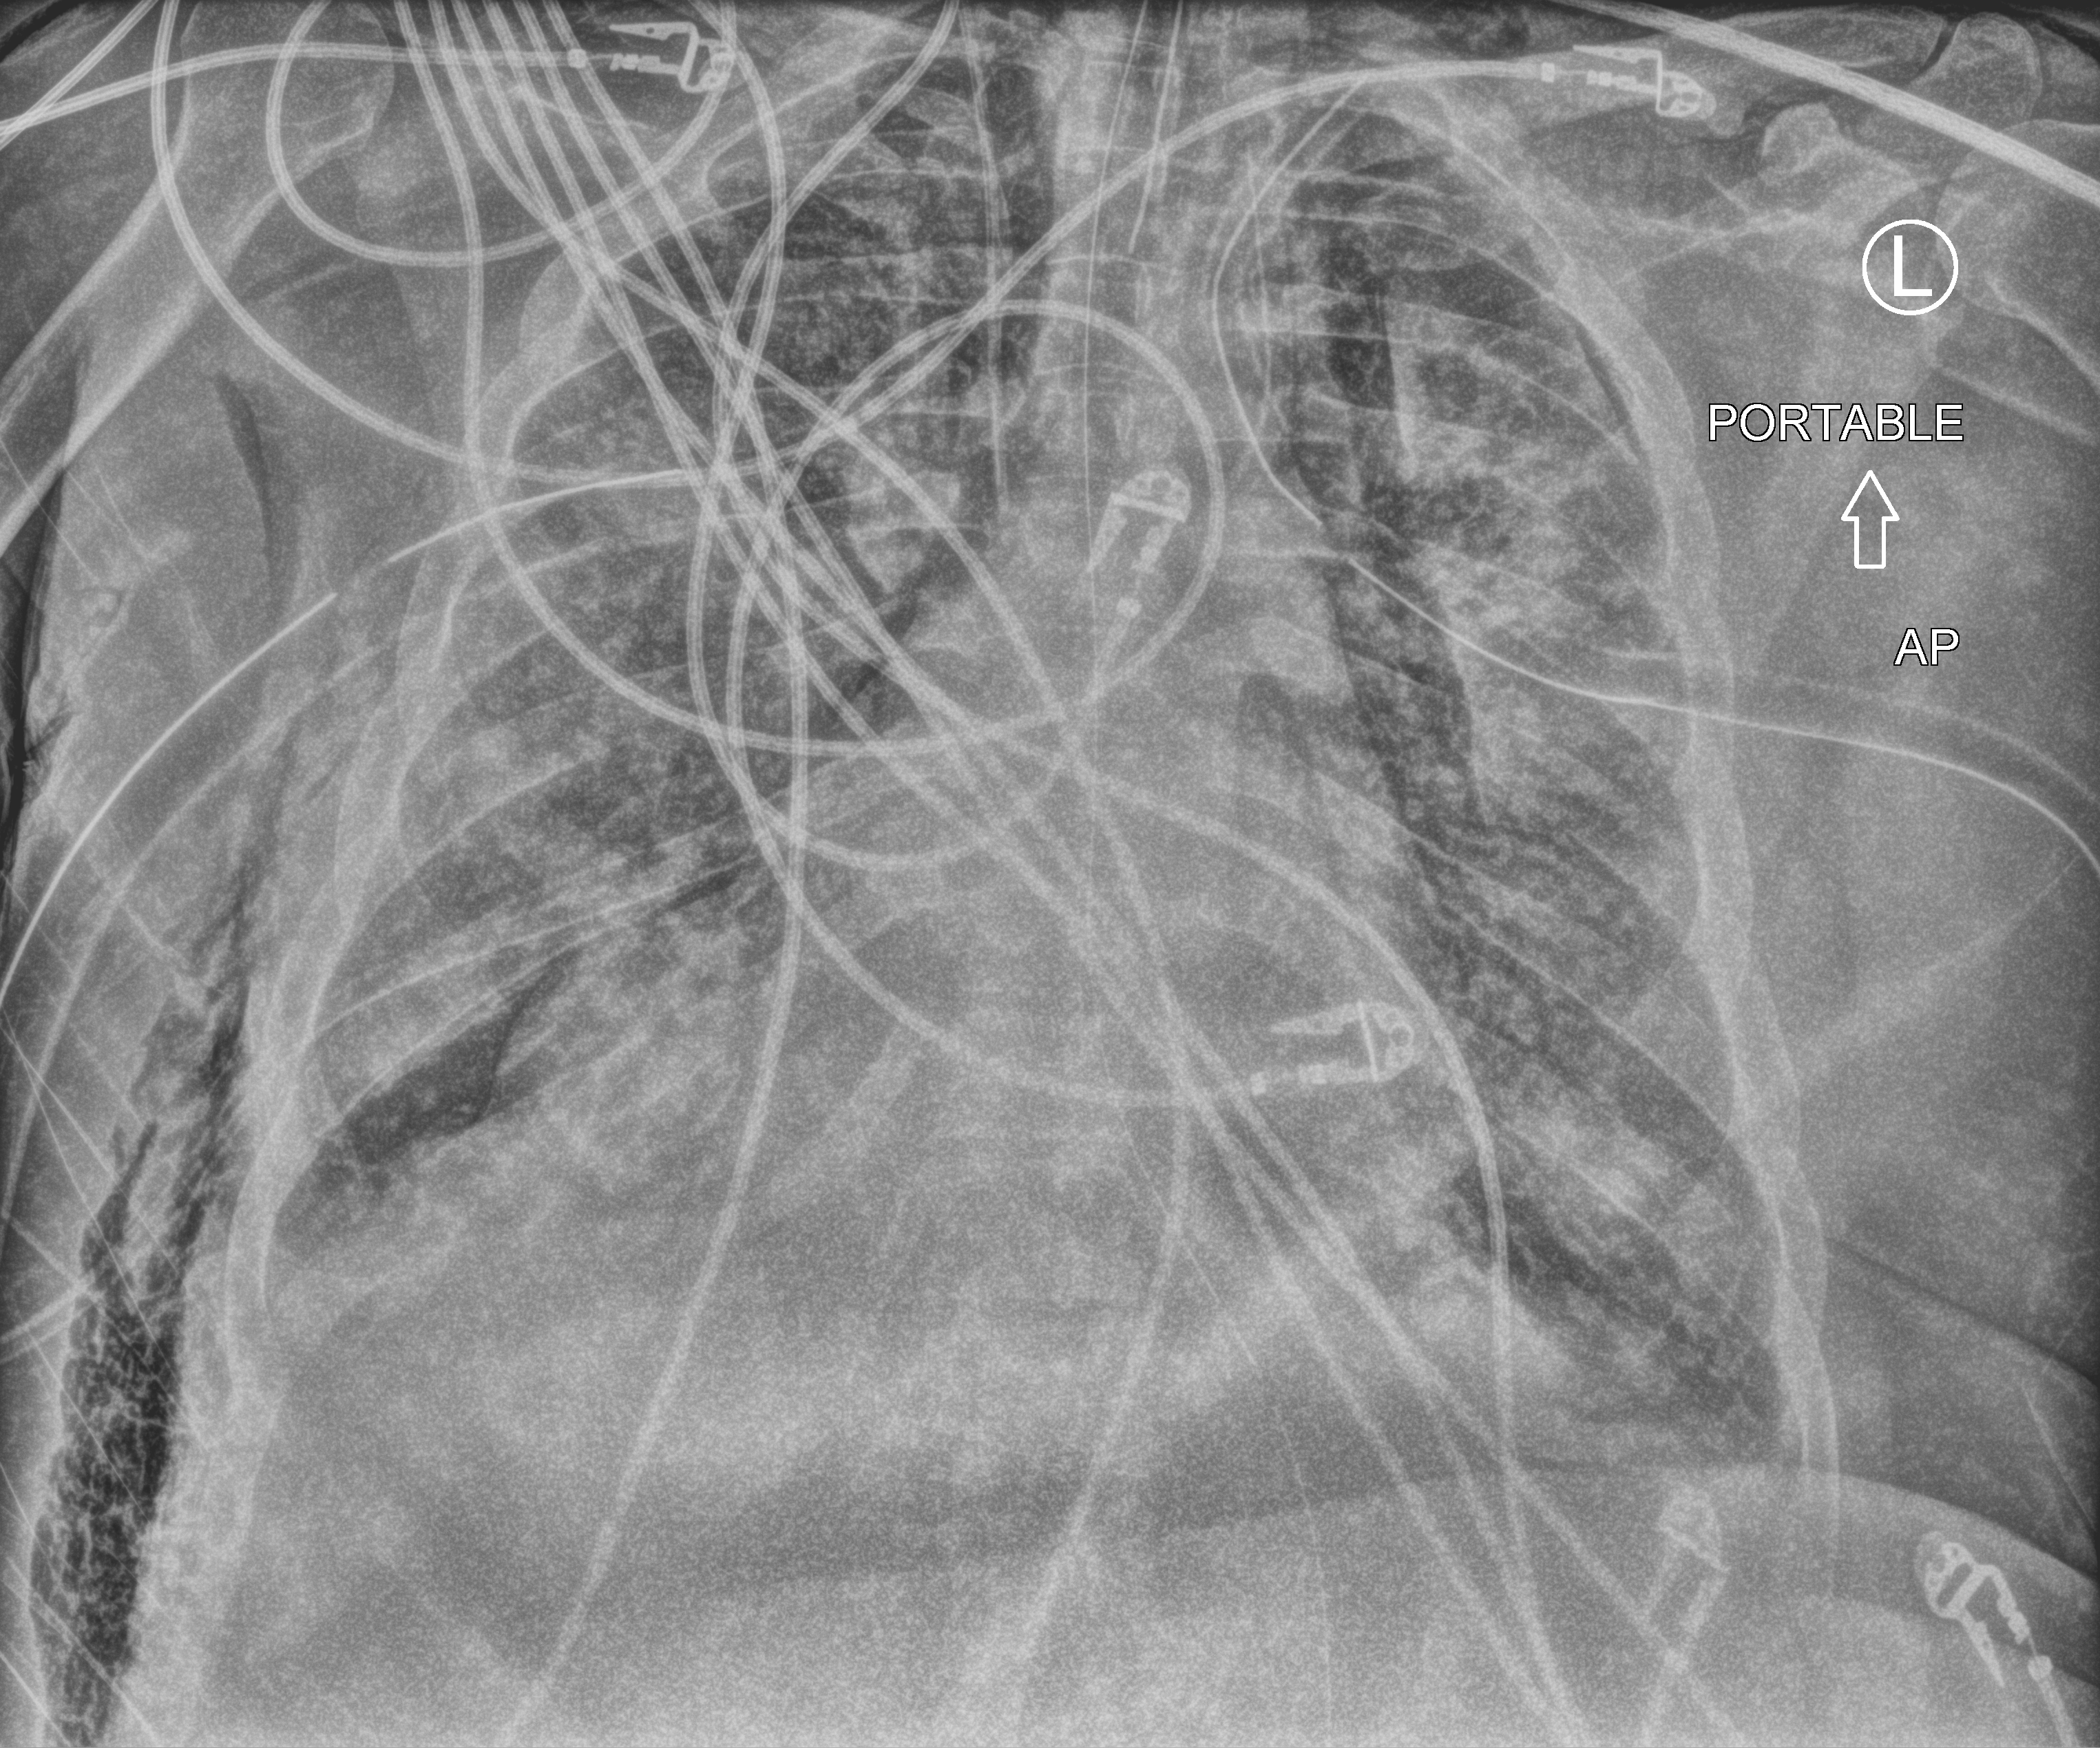
Bedside chest radiograph (computed radiography), anteroposterior (AP) projection. Patient hospitalised with COVID-19, aged 18–59 years.
Hospital-stay facts (about this admission, not read from this image; timing relative to this image not recorded):
- chronic kidney disease (admission record): no
- mechanically ventilated during this hospital stay: yes